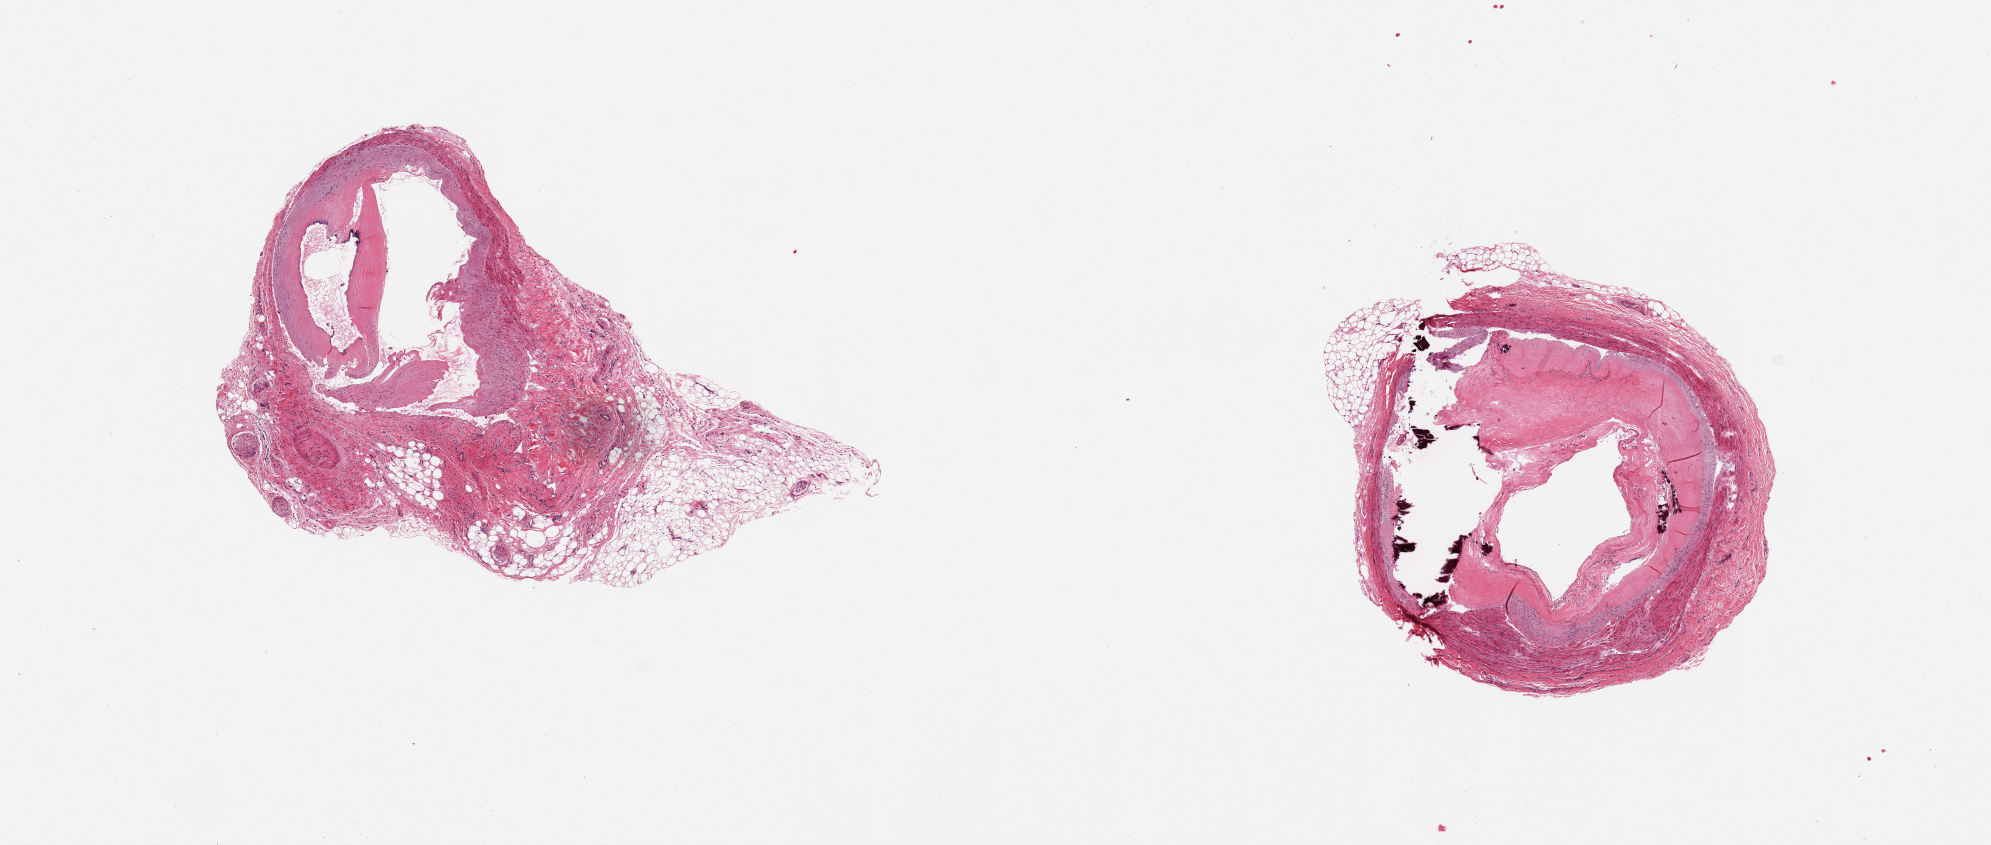
Whole-slide image, H&E stain, brightfield — a low-resolution overview of the entire scanned area, about 15.8 x 6.7 mm (acquisition: 20x scan); PAXgene-fixed paraffin-embedded (PFPE) section; target tissue: coronary artery; tissue donor sample. Female donor.
Pathologist's review note for this sample: 2 pieces, calcific atherosclerosis with narrowing of the lumen. 5% fat attached to one, second with ~40% fibroconnective tissue and nerve.